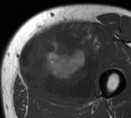
MRI of an extremity soft-tissue mass, one axial slice; slice 27 of 55 in the series (ordered by position); MR volume resampled by the dataset authors to the PET/CT grid (not the native acquisition matrix); 3.27 mm slice thickness; 131 × 118 image matrix, field of view 128 × 115 mm. Male patient. From the clinical record (not read from this slice): histological type: pleiomorphic liposarcoma; grade: high; site of the primary tumour: left thigh.
Annotated regions visible in this slice (expert contour drawn on MRI and transferred to this co-registered scan by the dataset authors):
- gross tumour volume including surrounding oedema: bounding box (x1, y1, x2, y2) in pixels: (16, 21, 104, 104)
- gross tumour volume (mass): (18, 21, 99, 104)